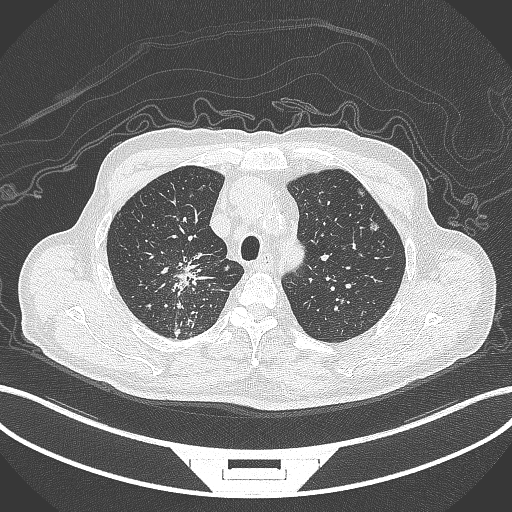
Chest CT, one axial slice; slice 298 of 407 in the series (ordered by position); reconstruction kernel B70f; 120 kVp; lung window (W 1500 / L -600 HU); 1 mm slice thickness; 512 × 512 image matrix, field of view 400 × 400 mm. Male patient, age 69 years. From the clinical record (not read from this slice): clinical TNM (as recorded): T1c N1 M1.
Outlined on this slice (bounding box drawn by a radiologist):
- lung tumour (recorded histology: adenocarcinoma): box from (x=165, y=254) to (x=213, y=307) px